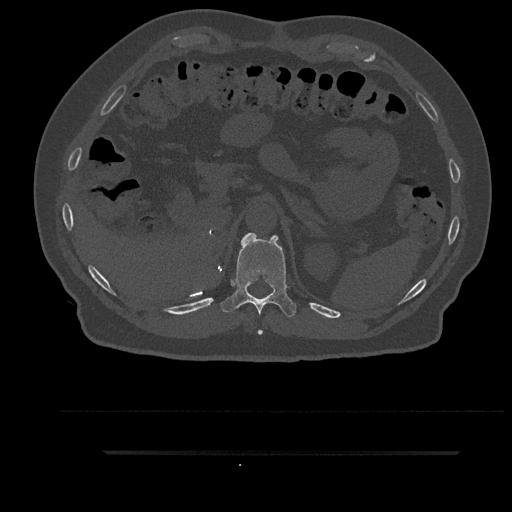
CT including the spine, one axial slice. Slice 305 of 797 in the series (ordered by position). Reconstruction kernel Br40s/3. 120 kVp. Bone window (W 1800 / L 400 HU). 0.5 mm slice thickness. 512 × 512 image matrix. Patient: male, 63 years. Case-level facts recorded for this patient, not image findings: primary cancer: renal; vertebrae with lytic lesions (as recorded): T8.
Structures marked on this image (semi-automatically segmented with operator editing):
- T11 vertebra: box from (x=220, y=233) to (x=296, y=335) px